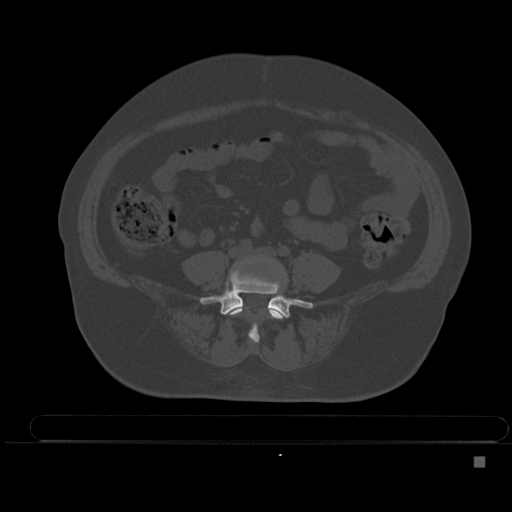
CT including the spine, one axial slice; slice 117 of 495 in the series (ordered by position); bone window (W 1800 / L 400 HU); 1.5 mm slice thickness; 512 × 512 image matrix, field of view 404 × 404 mm. Patient: female, 33 years. Case-level facts recorded for this patient, not image findings: primary cancer: breast; vertebrae with lytic lesions (as recorded): T1.
Structures marked on this image (semi-automatic segmentation, software-assisted and operator-edited):
- L4 vertebra: bounding box (x1, y1, x2, y2) in pixels: (229, 308, 286, 343)
- L5 vertebra: (200, 271, 313, 318)